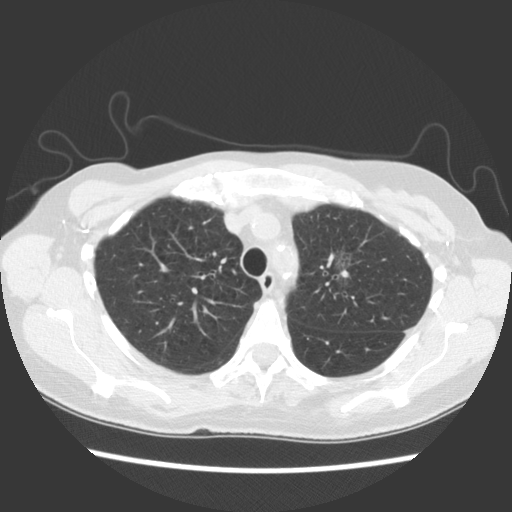
Axial slice from a low-dose chest CT screening exam, first (baseline) screen, lung window (W 1500 / L -600 HU), 140 kVp, slice 95 of 129 in the series, 512 × 512 image matrix, field of view 325 × 325 mm. Female, age 65 years at enrolment.
Expert-annotated lung lesion, box from (x=312, y=231) to (x=380, y=296) px. Screening reader's record for this exam (one nodule recorded; not confirmed to be the boxed lesion): non-calcified nodule or mass ≥4 mm, left upper lobe, 11 × 10 mm, poorly defined margins, ground glass attenuation. Official screen result: positive, change unspecified: nodule(s) >= 4 mm or enlarging nodule(s), mass(es), or other non-specific abnormalities suspicious for lung cancer. Participant outcome: lung cancer diagnosed 810 days after this screen (after the third annual screen) — adenocarcinoma, NOS, left upper lobe, moderately differentiated (G2), stage IA (AJCC 6th edition), 30 mm at pathology.